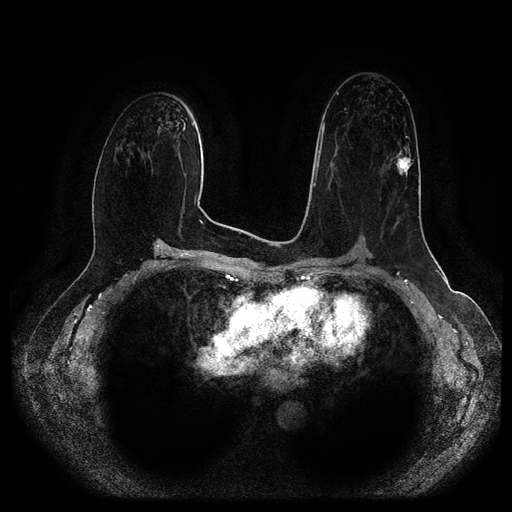
Breast MRI (dynamic contrast-enhanced, multi-phase), one axial slice. Position 59 of 116 along the scan axis. Dynamic contrast-enhanced series, time point 2 of 5 at this slice position (early post-contrast). 1.5 T. TE 2.6 ms, TR 5.2 ms. 2 mm slice thickness. 512 × 512 image matrix, field of view 380 × 380 mm. Patient: female, 57 years.
Outlined on this slice (semi-automatically segmented with operator editing):
- breast lesion (labelled 'tumour' in the annotation; benign lesions carry a separate 'benign' label): bounding box [x1, y1, x2, y2] px = [392, 151, 414, 177]